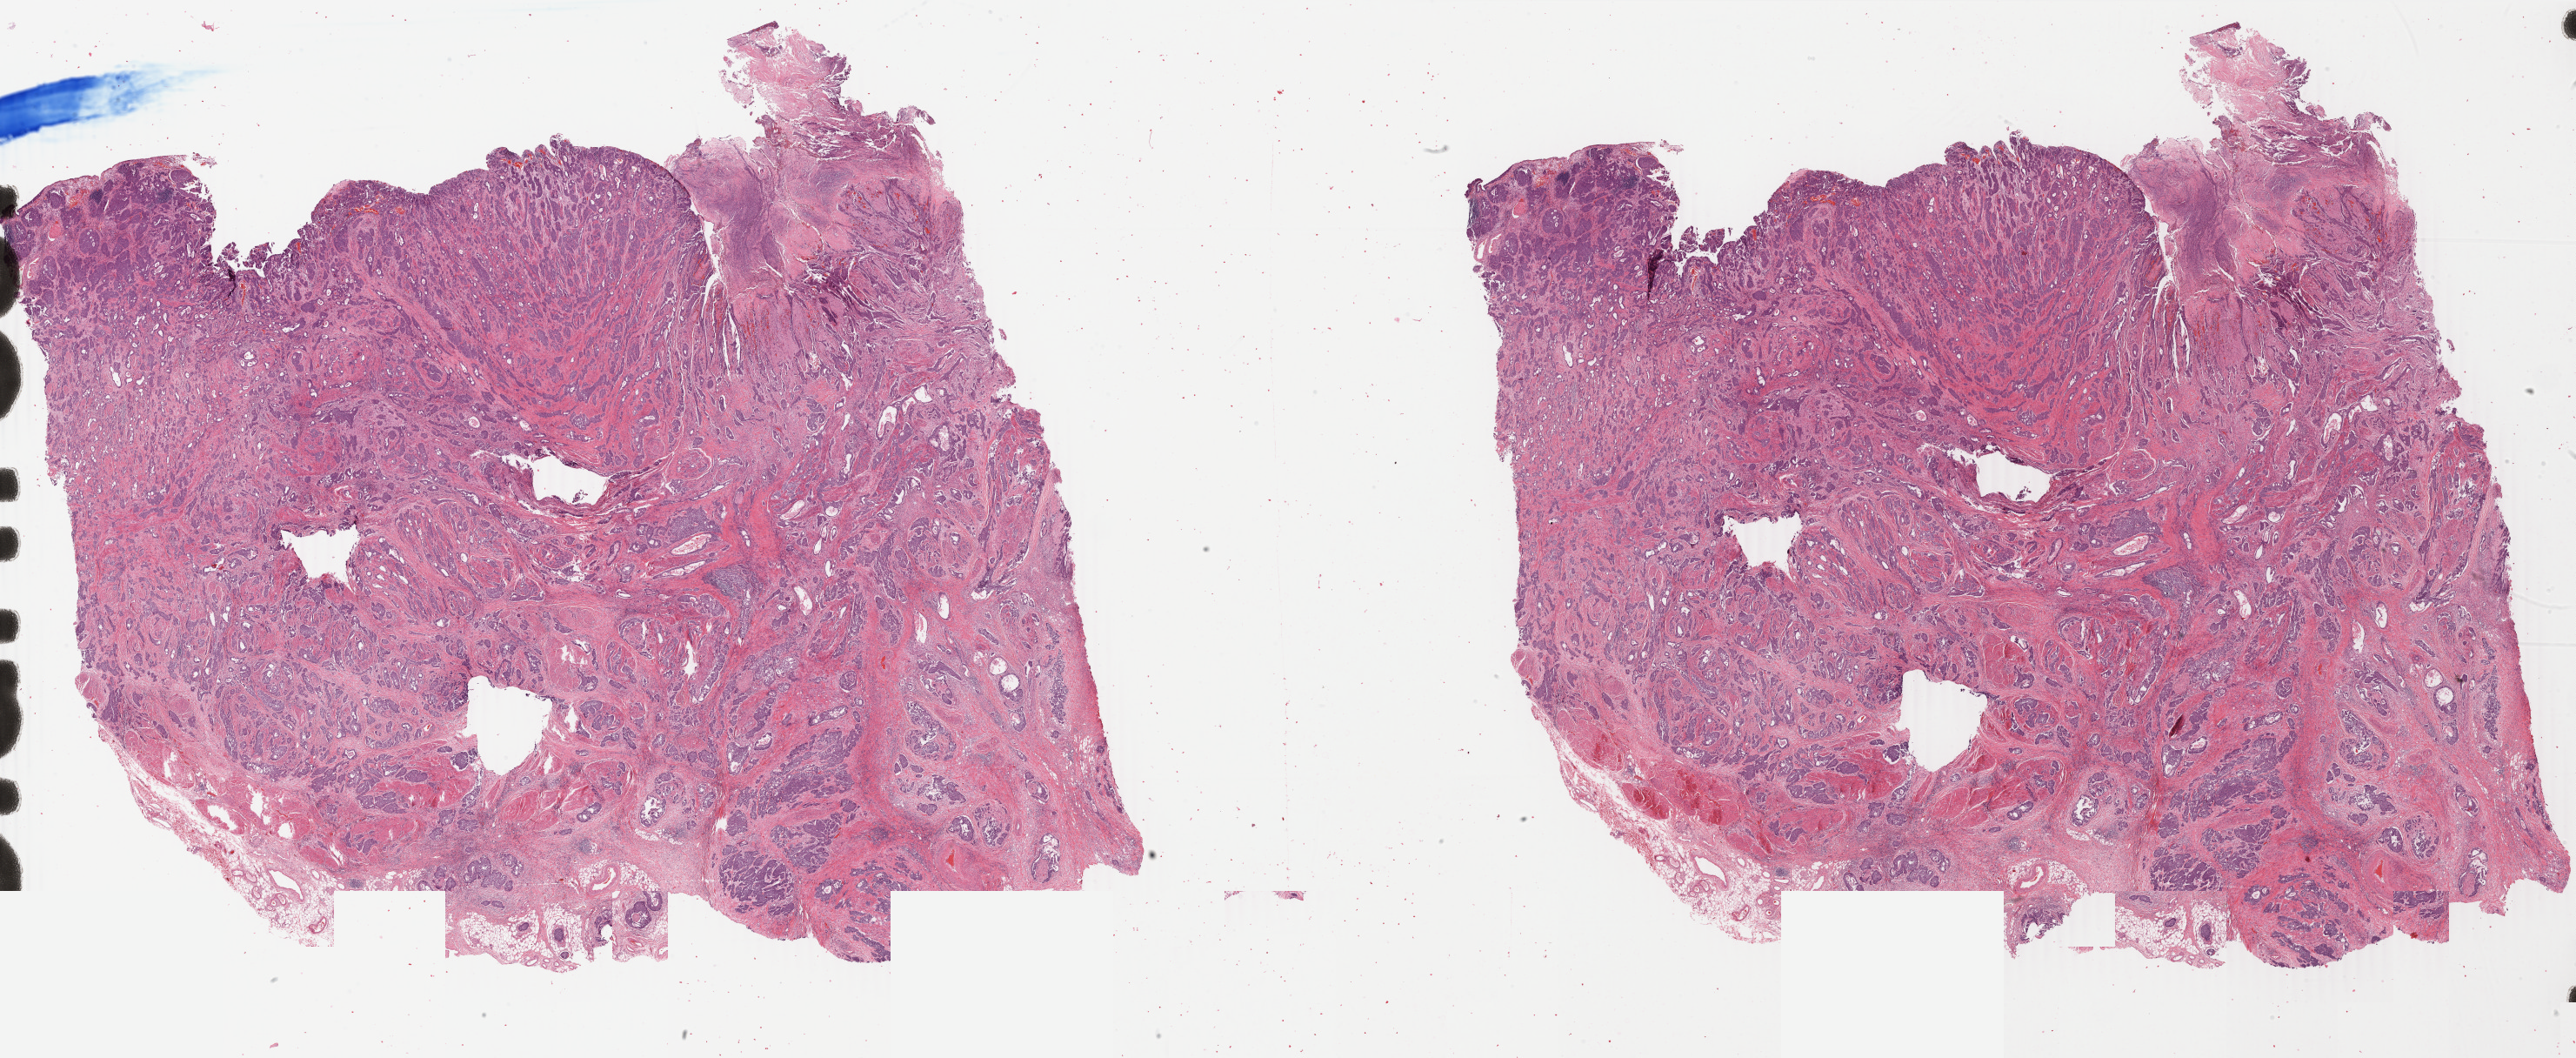
H&E whole-slide image, low-resolution overview of the scanned area, about 47.1 x 19.3 mm (acquisition: 40x scan), formalin-fixed paraffin-embedded (FFPE) diagnostic section, sample: primary tumour, bladder. Female patient; age at initial diagnosis 67 years. Histologic grade: high grade.
Lymph nodes positive (case pathology): 0 of 5 examined. TNM: T3a N0 MX. Pathologic diagnosis: Transitional cell carcinoma (posterior wall of bladder). AJCC pathologic stage: III (7th edition).